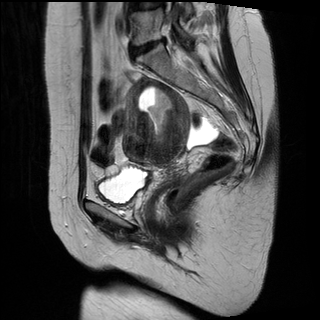
Pelvic MRI for cervical cancer, one sagittal slice. Position 19 of 34 along the scan axis. T2-weighted. 1.5 T. TE 89 ms, TR 3320 ms. 4 mm slice thickness. 320 × 320 image matrix. Female patient, age 49 years.
Outlined on this slice (manually delineated by an expert):
- uterus and cervix: bounding box (x1, y1, x2, y2) in pixels: (121, 75, 191, 168)